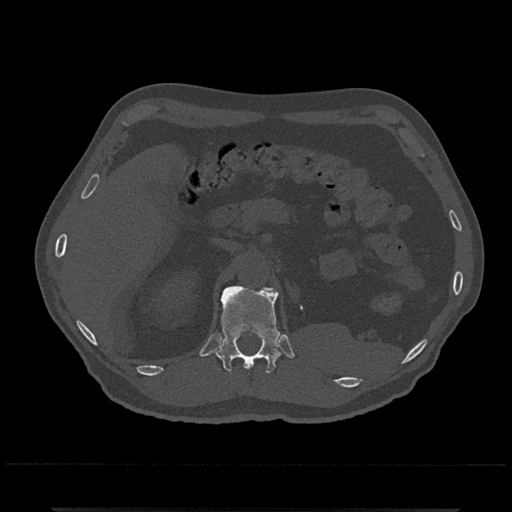
CT including the spine, one axial slice; slice 431 of 797 in the series (ordered by position); reconstruction kernel Br40s/3; bone window (W 1800 / L 400 HU); 0.5 mm slice thickness; 512 × 512 image matrix, field of view 393 × 393 mm. Patient: male, 67 years. Case-level facts recorded for this patient, not image findings: primary cancer: prostate.
Annotated regions visible in this slice (semi-automatically segmented with operator editing):
- T12 vertebra: bounding box [x1, y1, x2, y2] px = [214, 285, 281, 373]